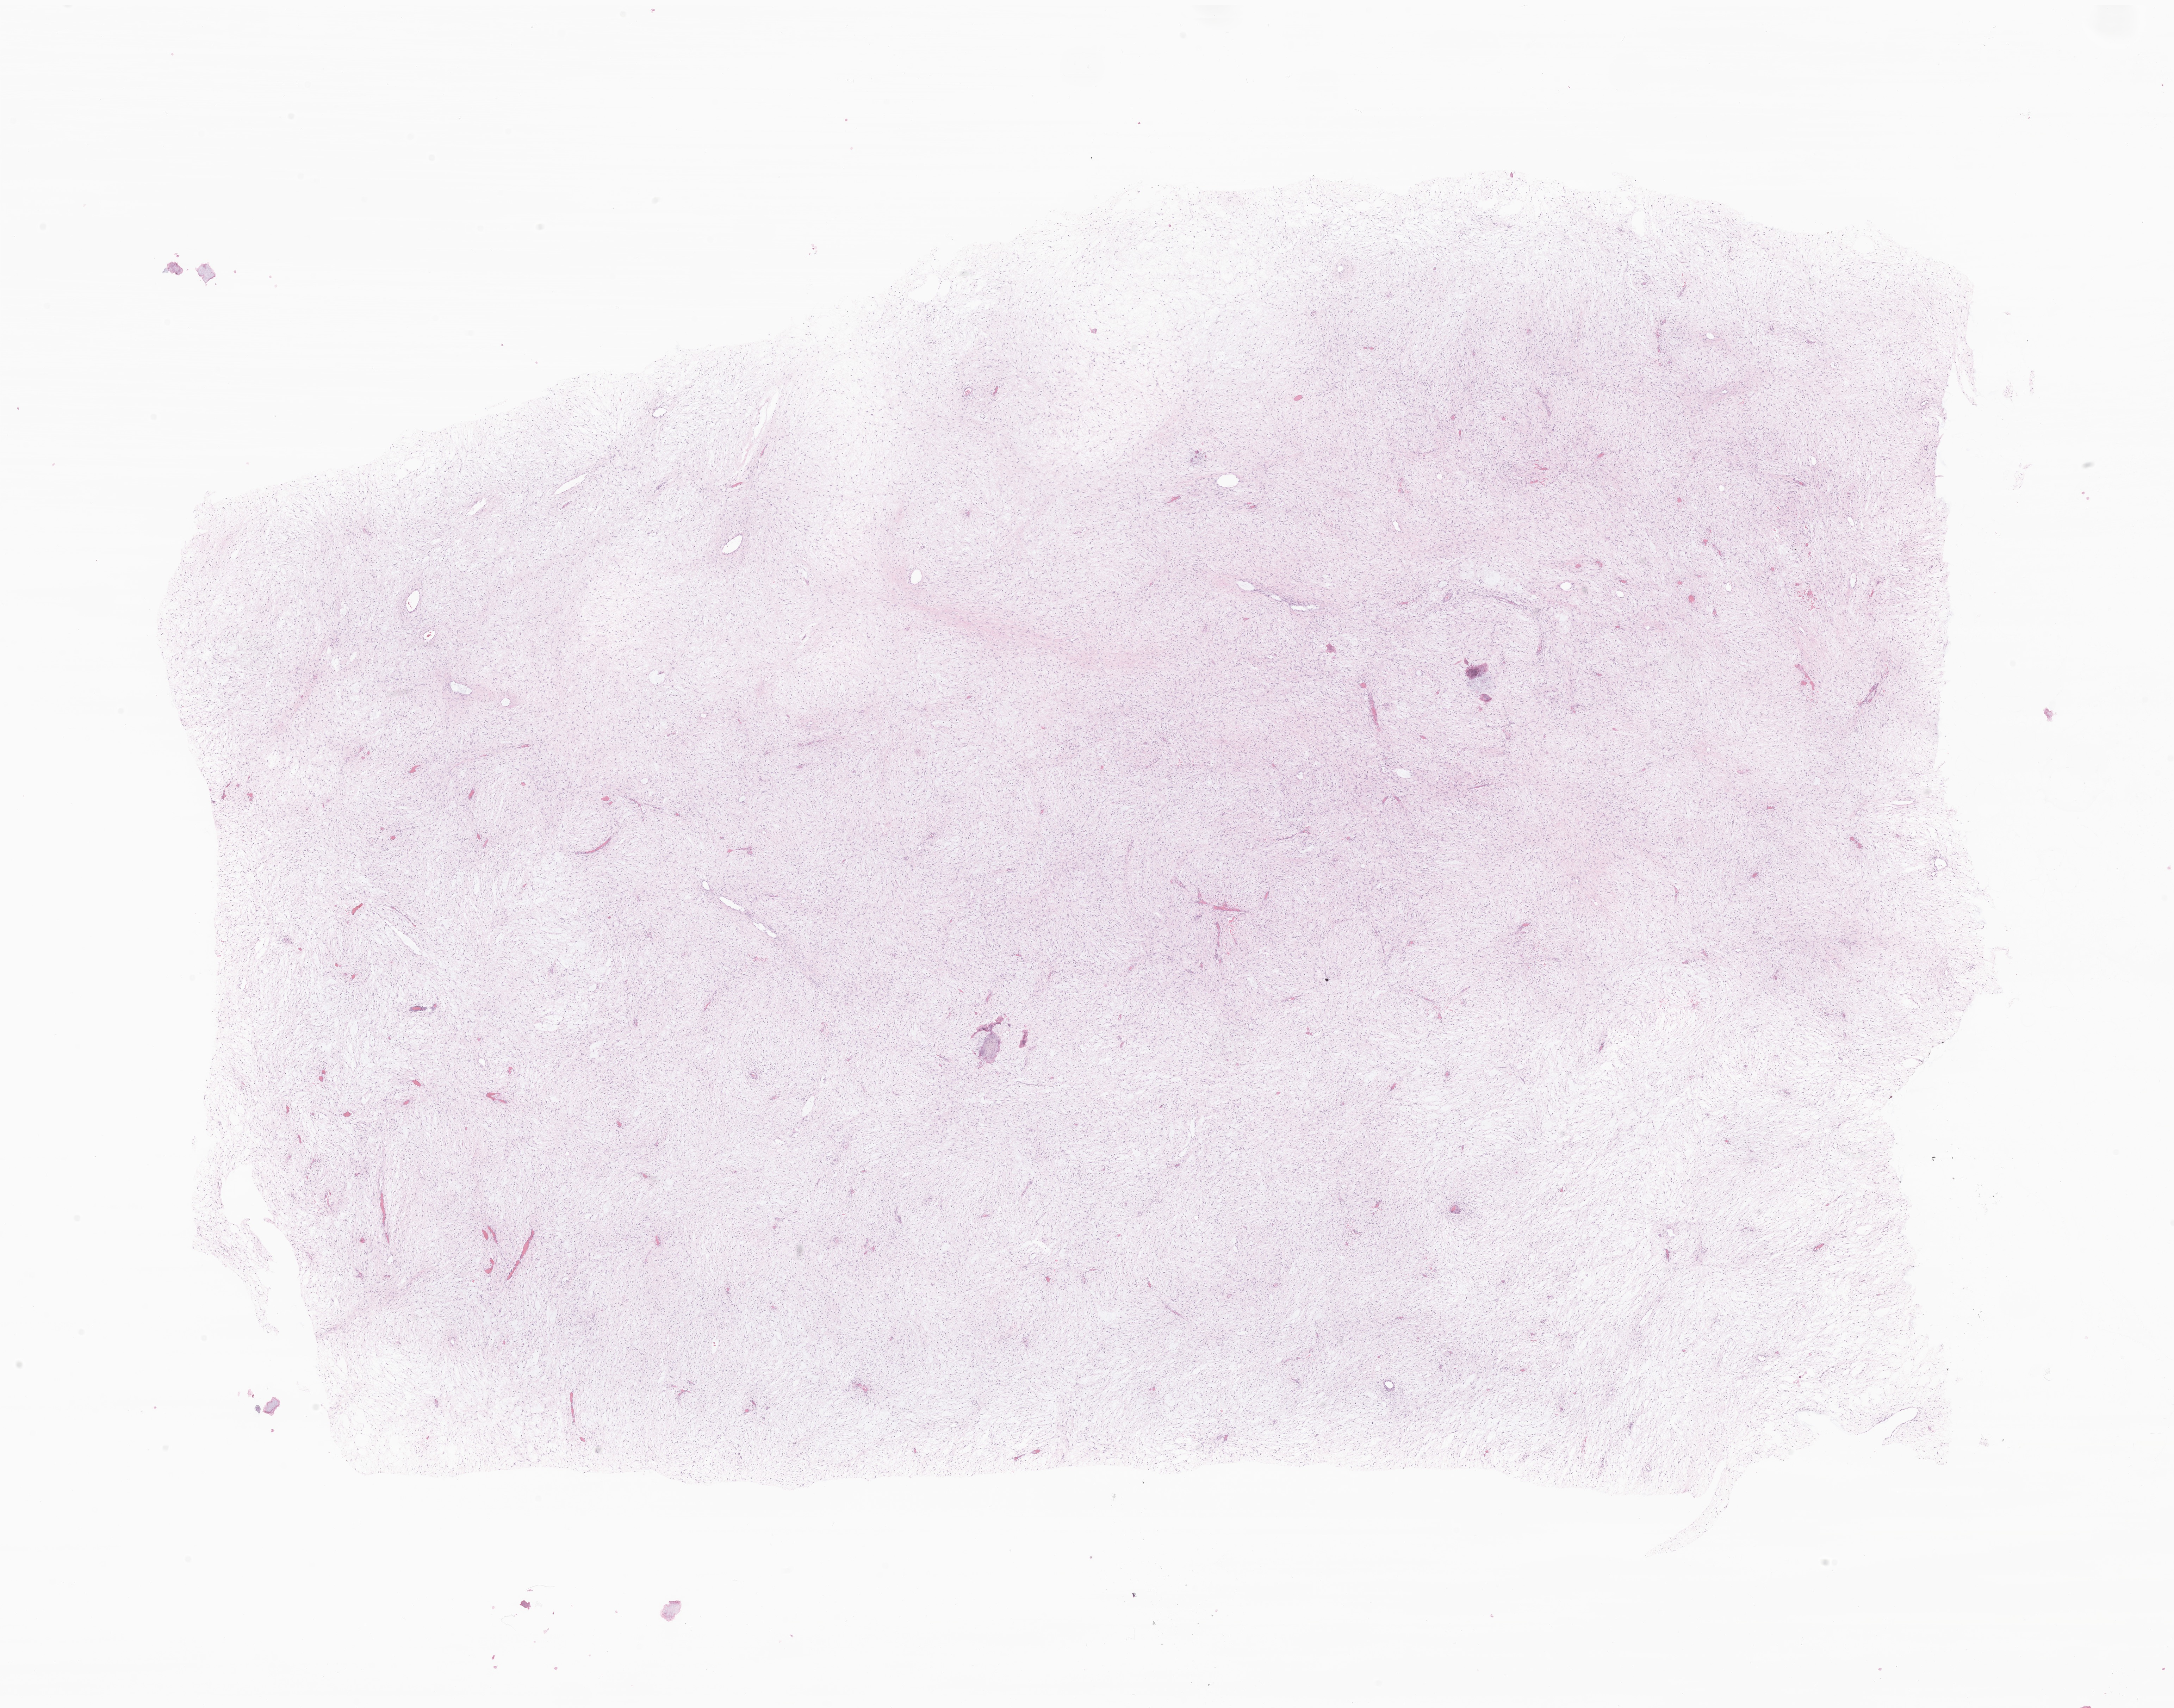
Hematoxylin and eosin (H&E) whole-slide image of tumor tissue from the abdomen — low-resolution overview of the scanned area, about 26.0 x 20.4 mm. Formalin-fixed, paraffin-embedded (FFPE) tissue. Male patient, age 206 months (17 years 2 months).
* diagnosis (ICD-O-3 morphology term): Sclerotic fibroma